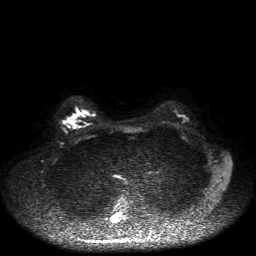
Breast MRI, one axial slice. Position 32 of 50 along the scan axis. Diffusion-weighted series; image 2 of 4 stored at this slice position (different b-values; order by instance number). 1.5 T. 4 mm slice thickness. 256 × 256 image matrix, field of view 360 × 360 mm. Female patient.
Annotated regions visible in this slice (manually delineated by an expert):
- tumour on diffusion-weighted imaging: bounding box <65,119,72,122> (left, top, right, bottom; pixels)